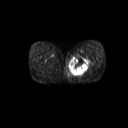
FDG PET of an extremity soft-tissue mass (from a PET/CT study), one axial slice; slice 25 of 267 in the series (ordered by position); 128 × 128 image matrix, field of view 600 × 600 mm. Male patient, age 59 years. Case-level facts recorded for this patient, not image findings: histological type: pleiomorphic liposarcoma; grade: high; site of the primary tumour: left thigh.
Outlined on this slice (expert contour drawn on MRI and transferred to this co-registered scan by the dataset authors):
- gross tumour volume including surrounding oedema: bounding box <70,55,92,76> (left, top, right, bottom; pixels)
- gross tumour volume (mass): <71,56,89,75>